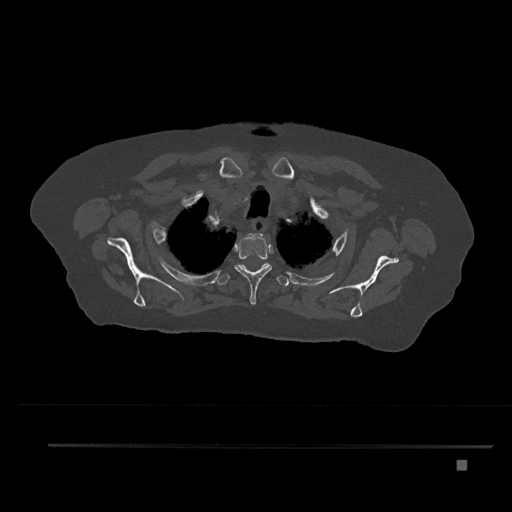
CT including the spine, one axial slice; position 663 of 797 along the scan axis; reconstruction kernel Br40s/3; 120 kVp; bone window (W 1800 / L 400 HU); 0.5 mm slice thickness; 512 × 512 image matrix, field of view 437 × 437 mm. Patient: female, 76 years. From the clinical record (not read from this slice): primary cancer: lung; vertebrae with lytic lesions (as recorded): T11, L3.
Annotated regions visible in this slice (semi-automatically segmented with operator editing):
- T1 vertebra: bounding box (x1, y1, x2, y2) in pixels: (250, 233, 265, 239)
- T2 vertebra: (234, 236, 272, 305)
- T3 vertebra: (218, 263, 289, 287)